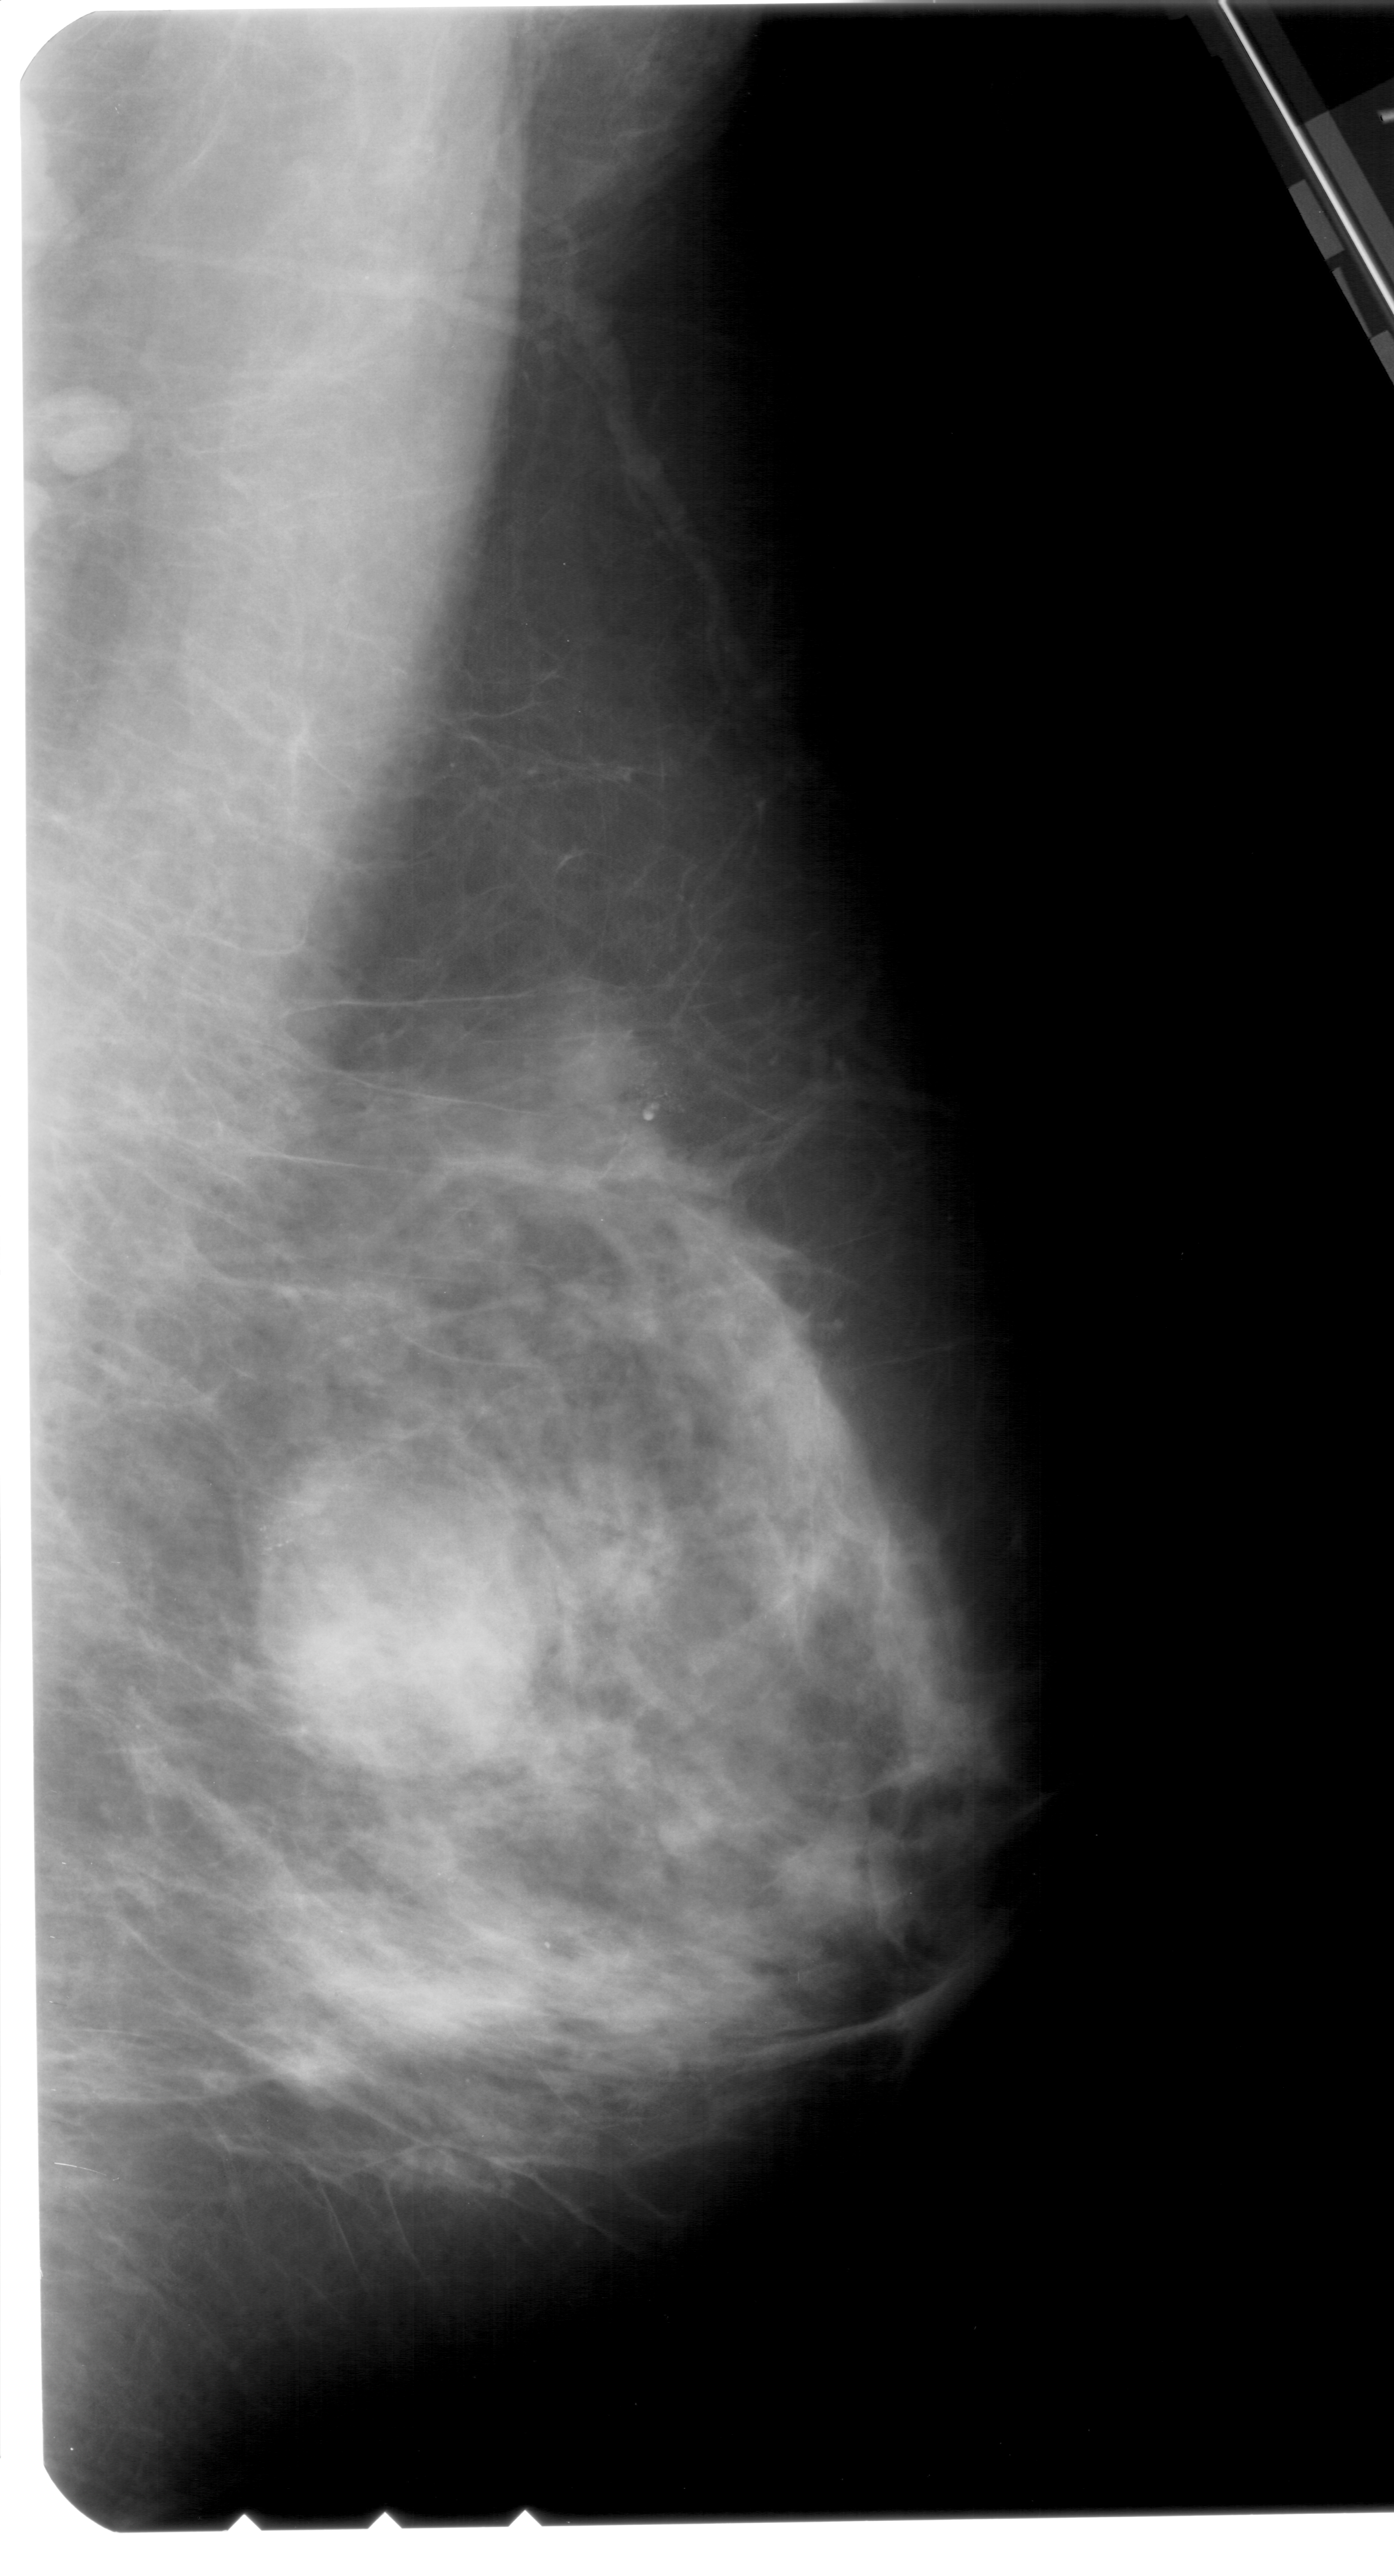
Scanned film-screen mammogram. Right breast. MLO view. BI-RADS breast density category 3 (scale 1–4). 1394 × 2576 image matrix.
Marked abnormalities (boxes around the expert regions of interest):
- calcifications, morphology pleomorphic, distribution clustered; BI-RADS assessment category 4; subtlety rating 2 on a 1 (subtle) to 5 (obvious) scale; pathology result (as recorded, not read from the image): benign: box from (x=208, y=1551) to (x=329, y=1654) px